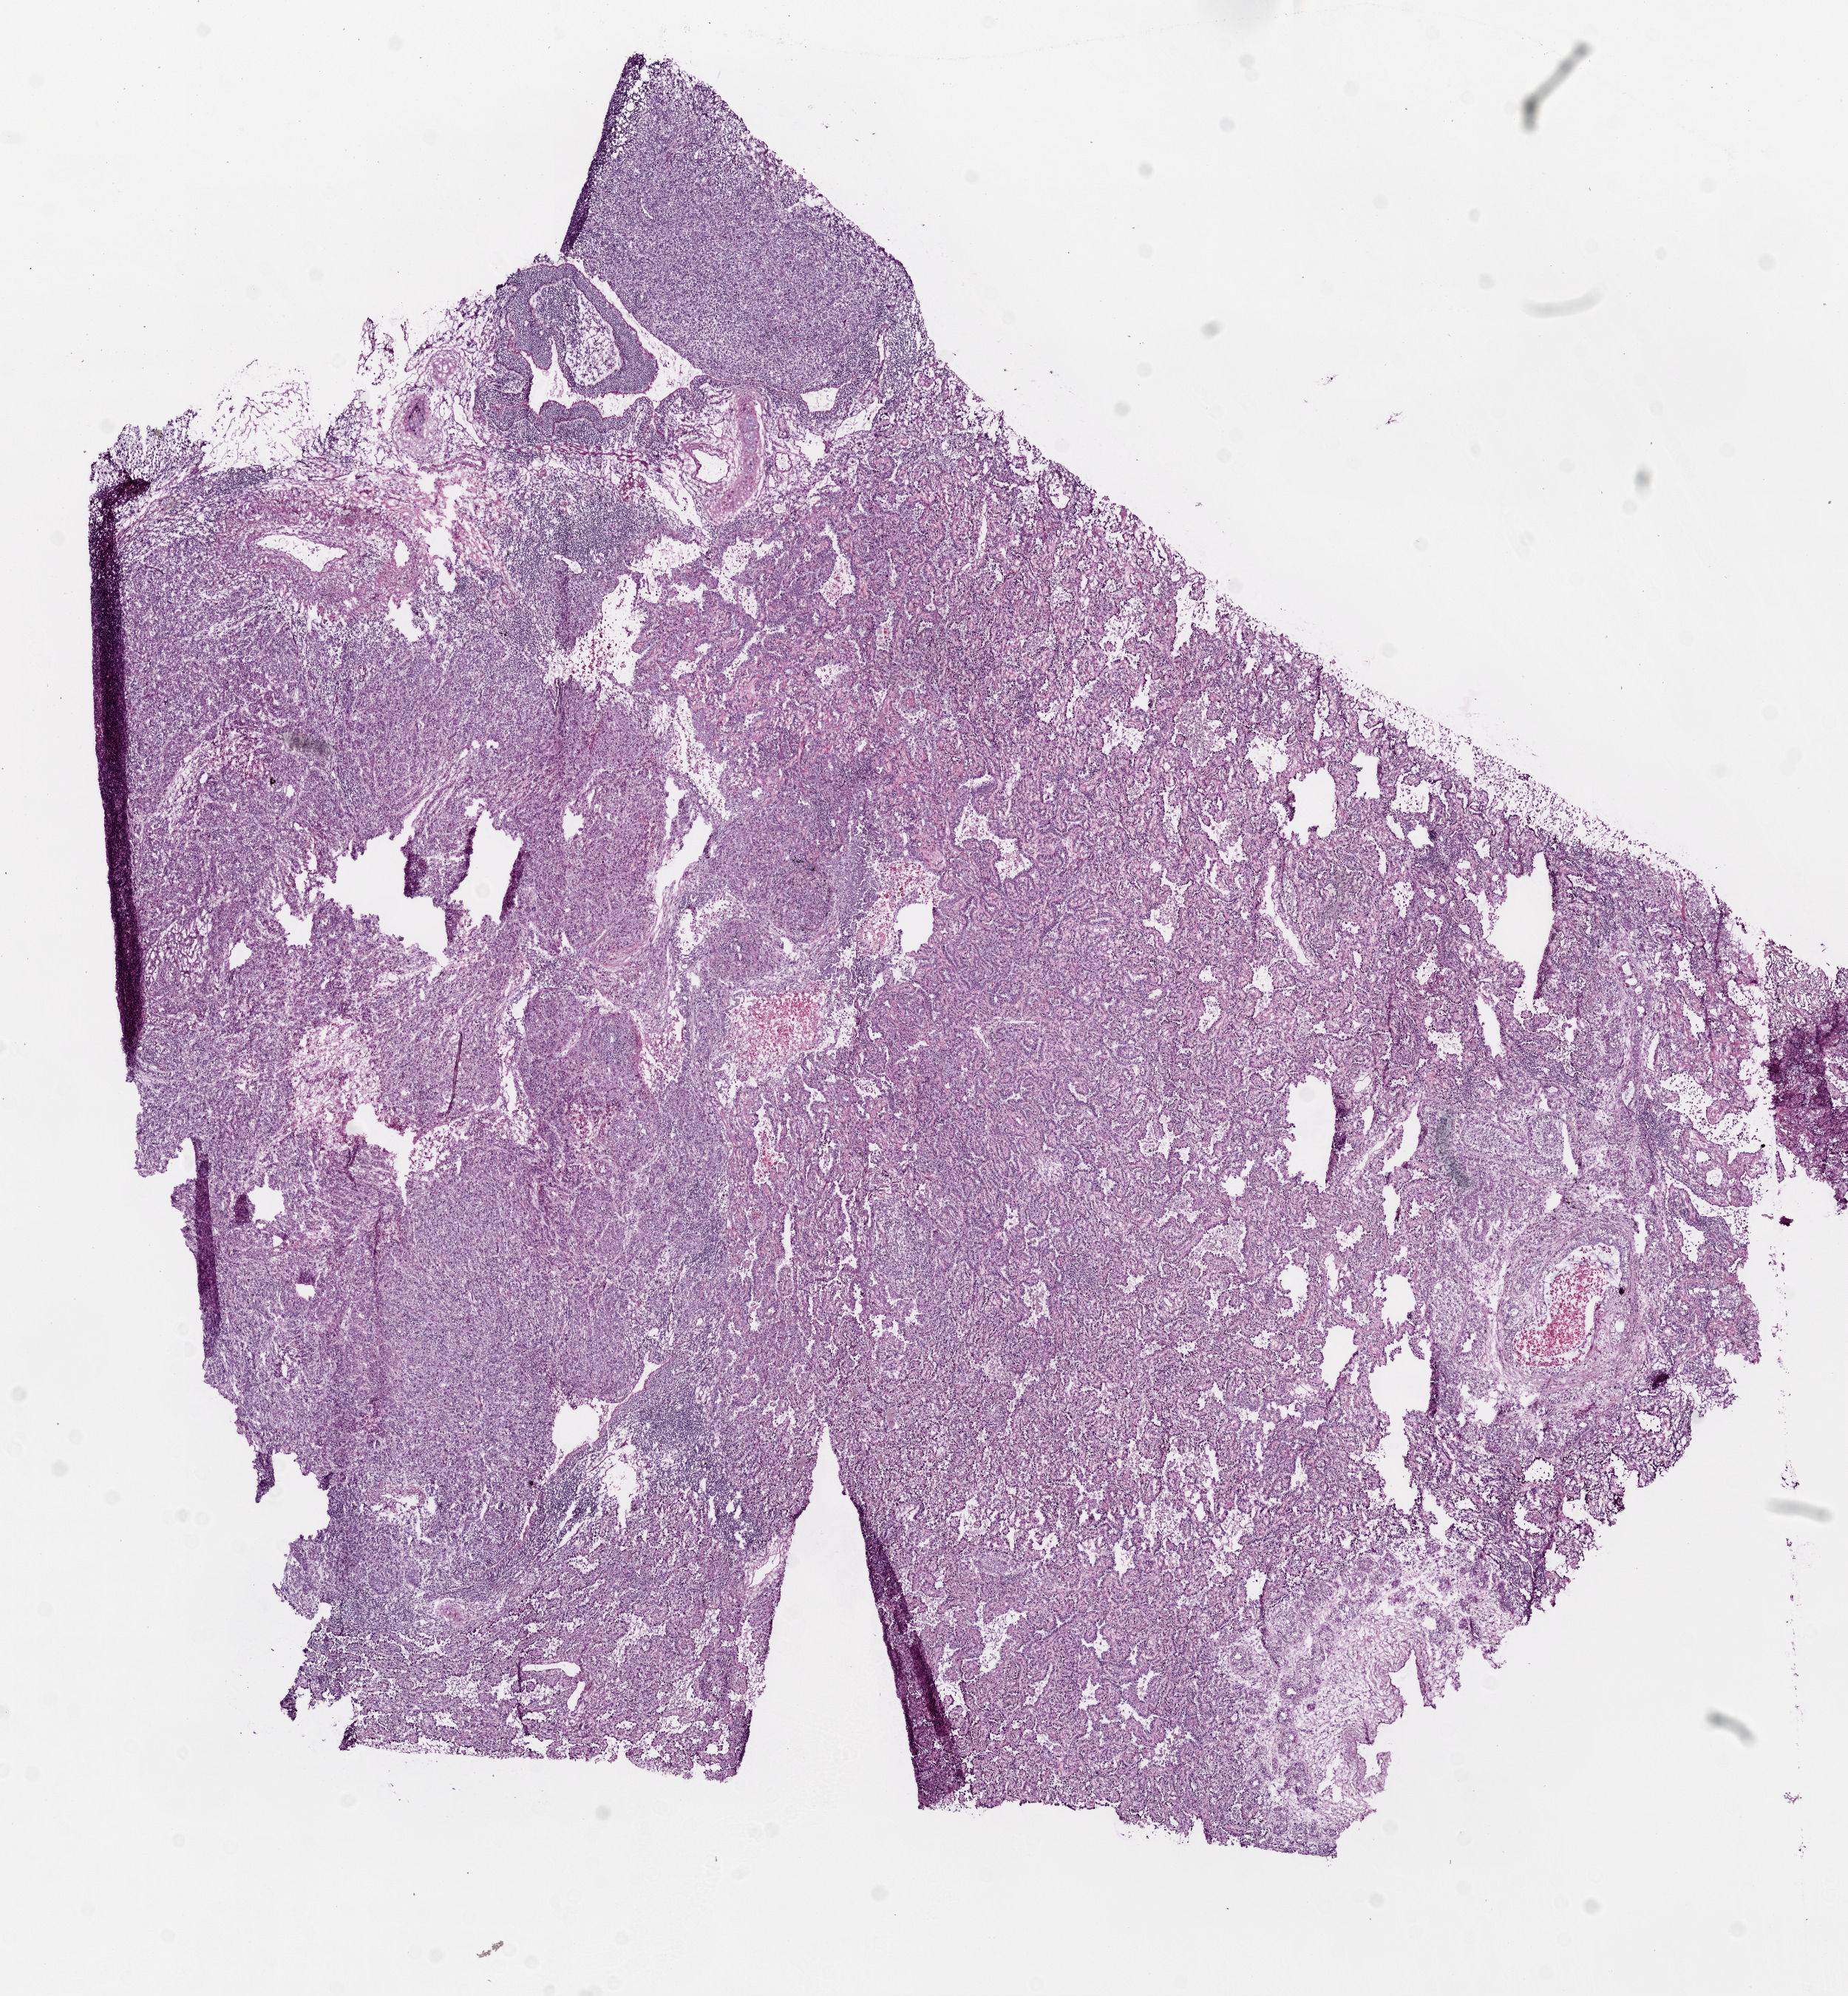
Digitized H&E tissue section (whole slide) — shown as a low-resolution overview of the whole scanned area (about 10.0 x 10.8 mm, from a 20x scan). Frozen section from the bottom of the tissue portion. Lung, primary tumour sample. Female, age 67 years at initial diagnosis. Pathologist review of this section (percent, as recorded): tumour cells 65%, tumour nuclei 70%, normal cells 5%, stromal cells 25%, necrosis 5%.
AJCC pathologic stage: IV (6th edition). Diagnosis: Adenocarcinoma with mixed subtypes (lower lobe, lung).